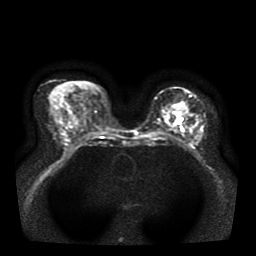
Breast MRI, one axial slice. Slice 20 of 39 in the series (ordered by position). Diffusion-weighted series; image 2 of 4 stored at this slice position (different b-values; order by instance number). 1.5 T. 5 mm slice thickness. 256 × 256 image matrix, field of view 330 × 330 mm. Female patient.
Outlined on this slice (outlined manually by an expert reader):
- tumour on diffusion-weighted imaging: box from (x=178, y=103) to (x=191, y=120) px